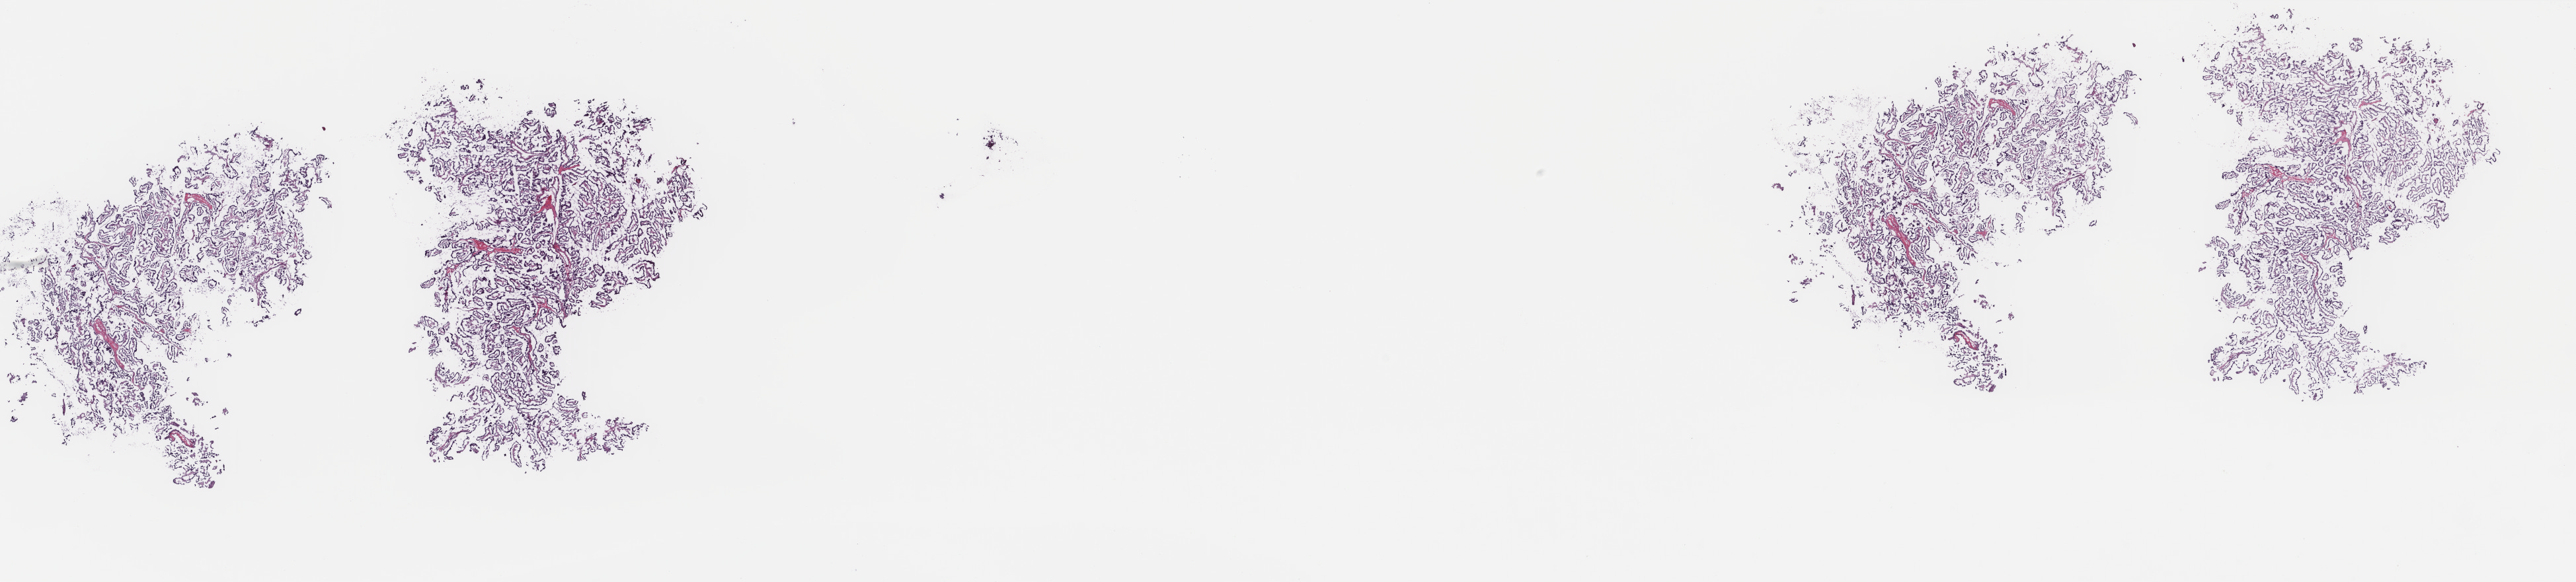
Digitized H&E-stained tissue section (whole slide), low-resolution overview of the scanned area, about 30.9 x 7.0 mm (from a 40x scan). Frozen section from the top of the tissue portion. Sample: primary tumour, thyroid. Female patient; age at initial diagnosis 21 years. Slide review estimates, as recorded: tumour cells 100%, tumour nuclei 85%.
Histologic diagnosis: Papillary adenocarcinoma, NOS (thyroid gland).